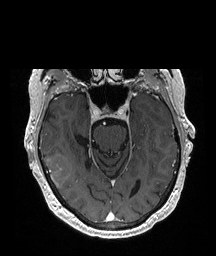
Brain MRI from a brain-tumour surgery series, one axial slice; T1-weighted post-contrast; 1 mm slice thickness; 216 × 256 image matrix. From the clinical record (not read from this slice): histopathology: Glioblastoma; WHO grade: 4; IDH mutation: no; tumour location: Right Temporal.
Structures marked on this image (expert manual segmentation):
- tumour: box from (x=45, y=154) to (x=72, y=188) px